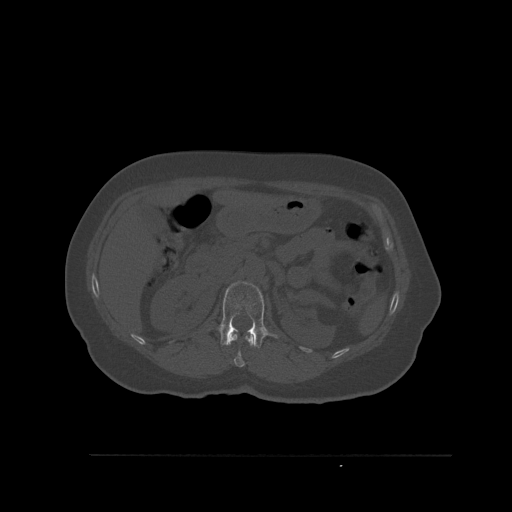
CT including the spine, one axial slice. Position 269 of 527 along the scan axis. Bone window (W 1800 / L 400 HU). 1.5 mm slice thickness. 512 × 512 image matrix, field of view 470 × 470 mm. Female patient, age 73 years. From the clinical record (not read from this slice): primary cancer: breast.
Structures marked on this image (semi-automatic segmentation, software-assisted and operator-edited):
- L1 vertebra: bounding box (x1, y1, x2, y2) in pixels: (219, 281, 278, 348)
- T12 vertebra: (228, 334, 254, 367)